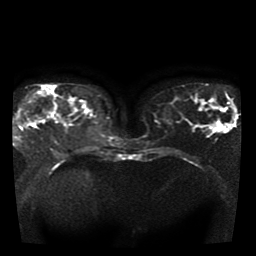
Breast MRI, one axial slice. Diffusion-weighted series; image 2 of 4 stored at this slice position (different b-values; order by instance number). 1.5 T. 5 mm slice thickness. 256 × 256 image matrix. Female patient.
Annotated regions visible in this slice (manually delineated by an expert):
- tumour on diffusion-weighted imaging: bounding box [x1, y1, x2, y2] px = [22, 117, 38, 126]